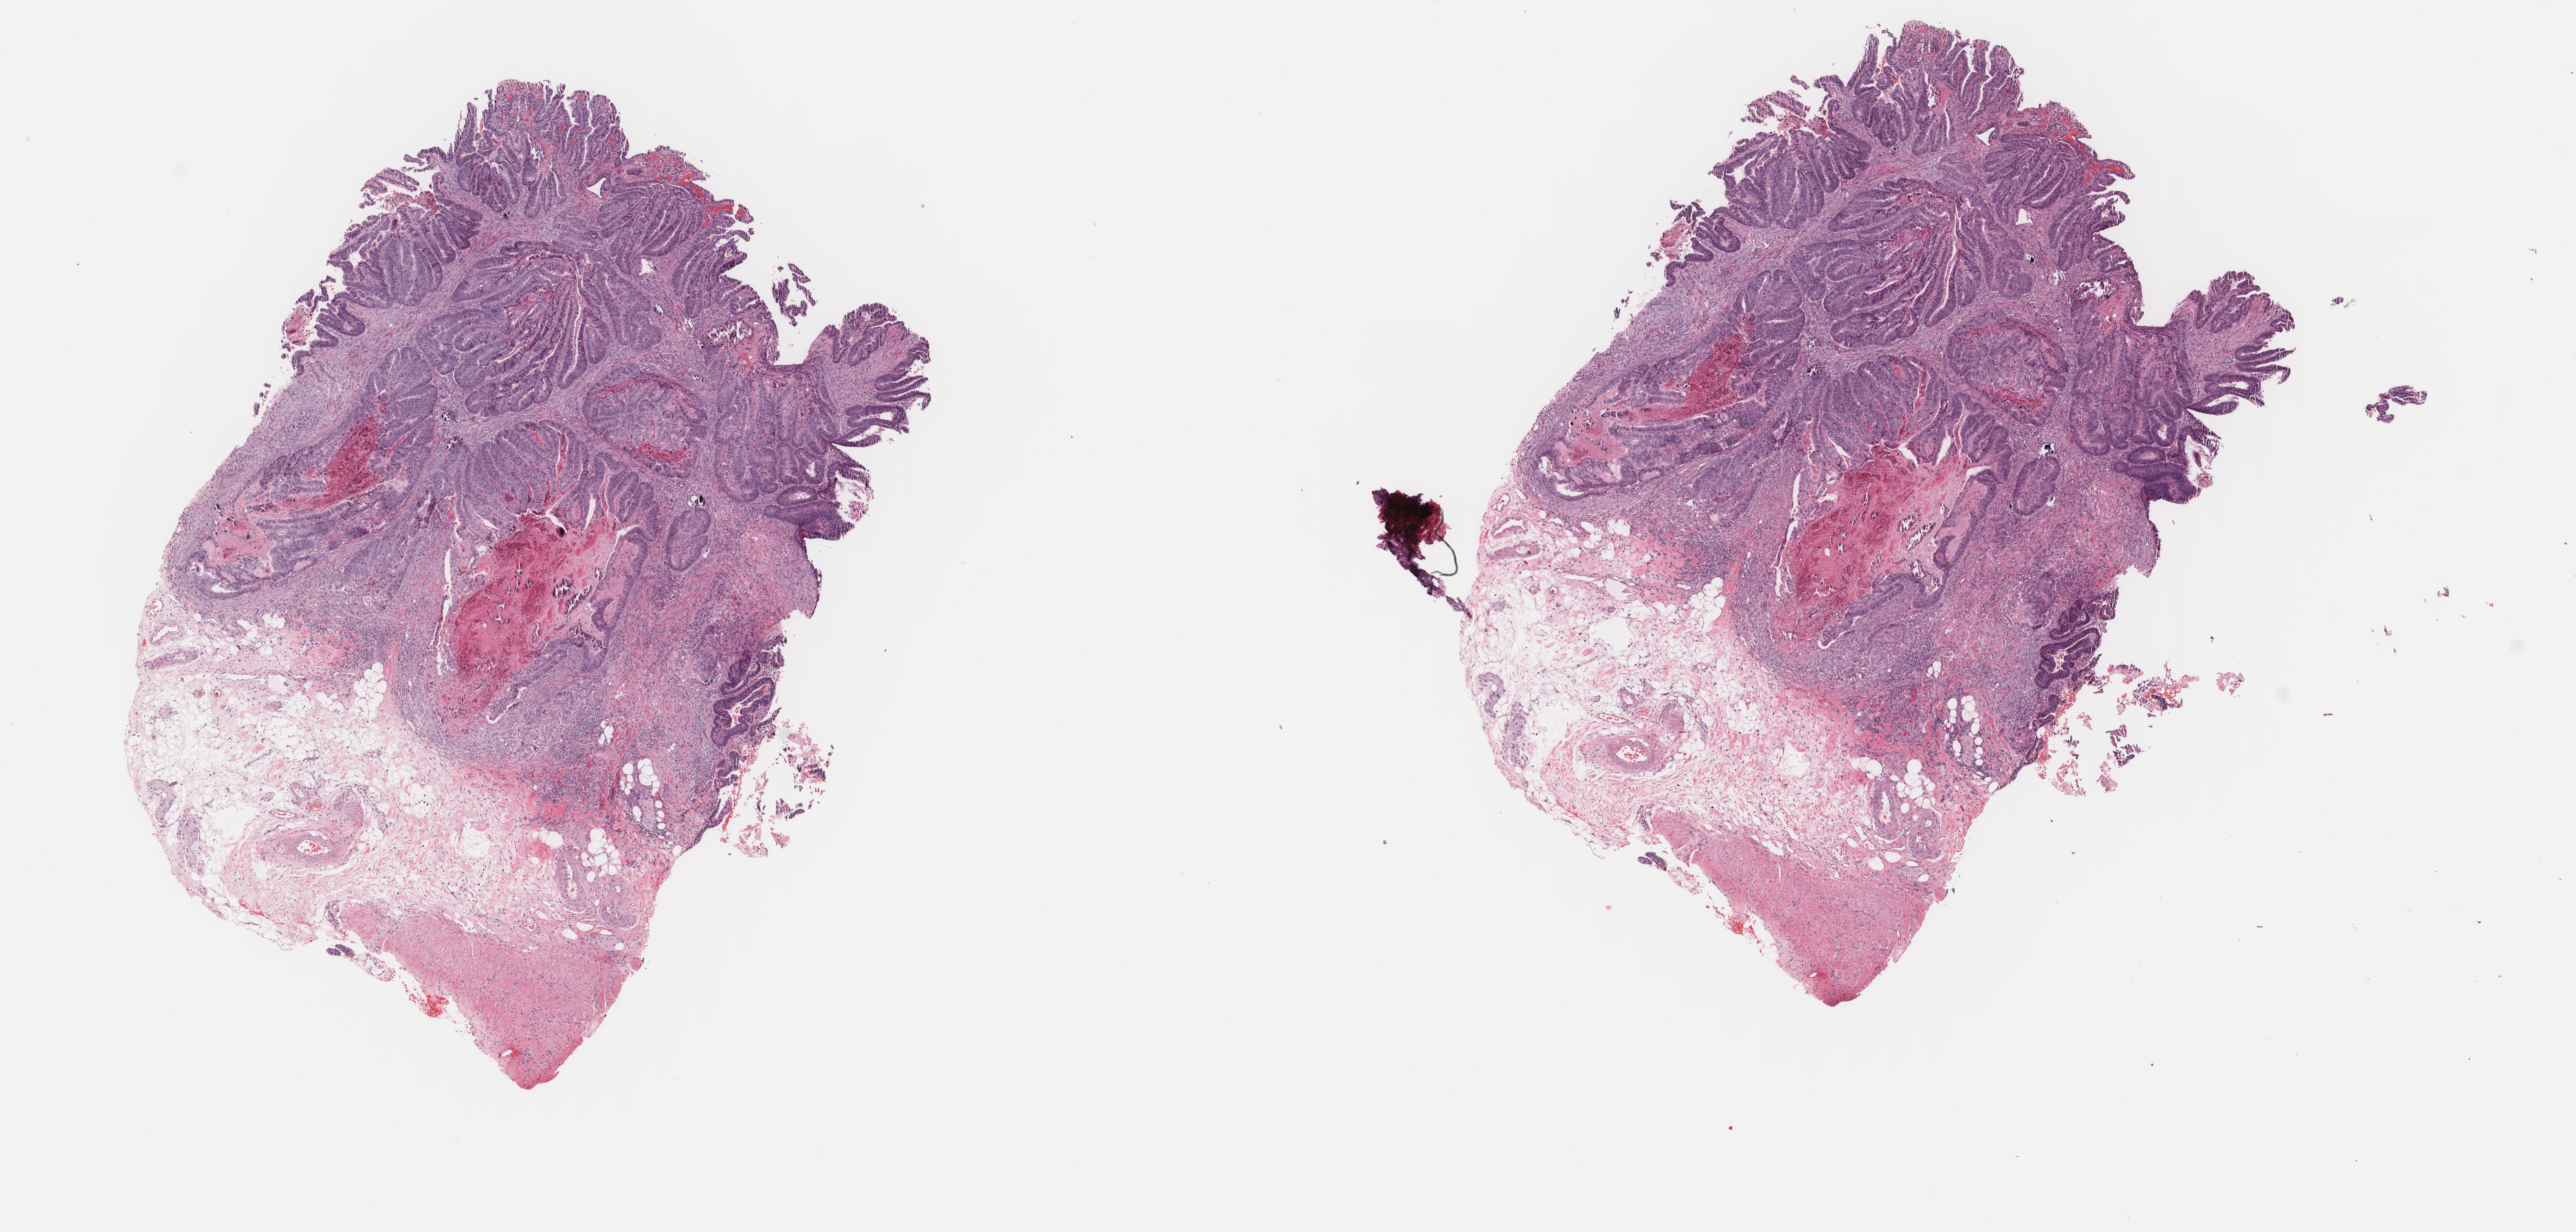
H&E whole-slide image — whole scanned area (about 14.9 x 7.1 mm, slide scanned at 40x) shown as a low-resolution overview, frozen section, sample: primary tumour, colon. Male, age 74 years at initial diagnosis. Pathologist review of this section (percent, as recorded): tumour cells 40%, tumour nuclei 40%, normal cells 0%, stromal cells 50%, necrosis 10%. Infiltration values recorded for this section: lymphocyte infiltration 0%, monocyte infiltration 0%, neutrophil infiltration 0%.
TNM: T2 N0 M0. Diagnosis: Adenocarcinoma, NOS. AJCC pathologic stage: I. Lymph nodes positive (case pathology): 0 of 16 examined.